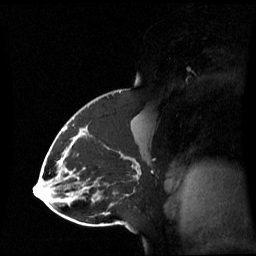
Breast MRI (dynamic contrast-enhanced), one sagittal slice; slice 36 of 60 in the series (ordered by position); dynamic contrast-enhanced series, image 2 of 3 at this slice position (ordered by acquisition); 1.5 T; TE 4.2 ms, TR 8.4 ms; 2.8 mm slice thickness; 256 × 256 image matrix, field of view 270 × 270 mm. Patient: female, 43 years. Case-level facts recorded for this patient, not image findings: setting: breast cancer imaged before/during neoadjuvant chemotherapy; receptor status: triple-negative.
Annotated regions visible in this slice (semi-automatic segmentation, software-assisted and operator-edited):
- analysis volume of interest (the breast-tissue region the enhancement analysis was run in; not a lesion): box from (x=65, y=118) to (x=143, y=198) px
- tumour enhancement mask (voxels above the 70 % enhancement threshold inside the analysis volume of interest): (x=65, y=127)–(x=129, y=174)